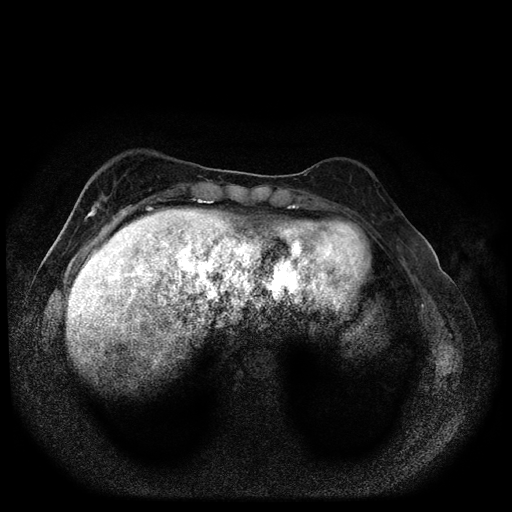
Breast MRI (dynamic contrast-enhanced, multi-phase), one axial slice; dynamic contrast-enhanced series, time point 2 of 5 at this slice position (early post-contrast); 1.5 T; TE 2.7 ms, TR 5.4 ms; 2 mm slice thickness; 512 × 512 image matrix. Female patient, age 49 years.
Structures marked on this image (semi-automatic segmentation, software-assisted and operator-edited):
- breast lesion (labelled 'tumour' in the annotation; benign lesions carry a separate 'benign' label): bounding box (x1, y1, x2, y2) in pixels: (82, 201, 102, 221)